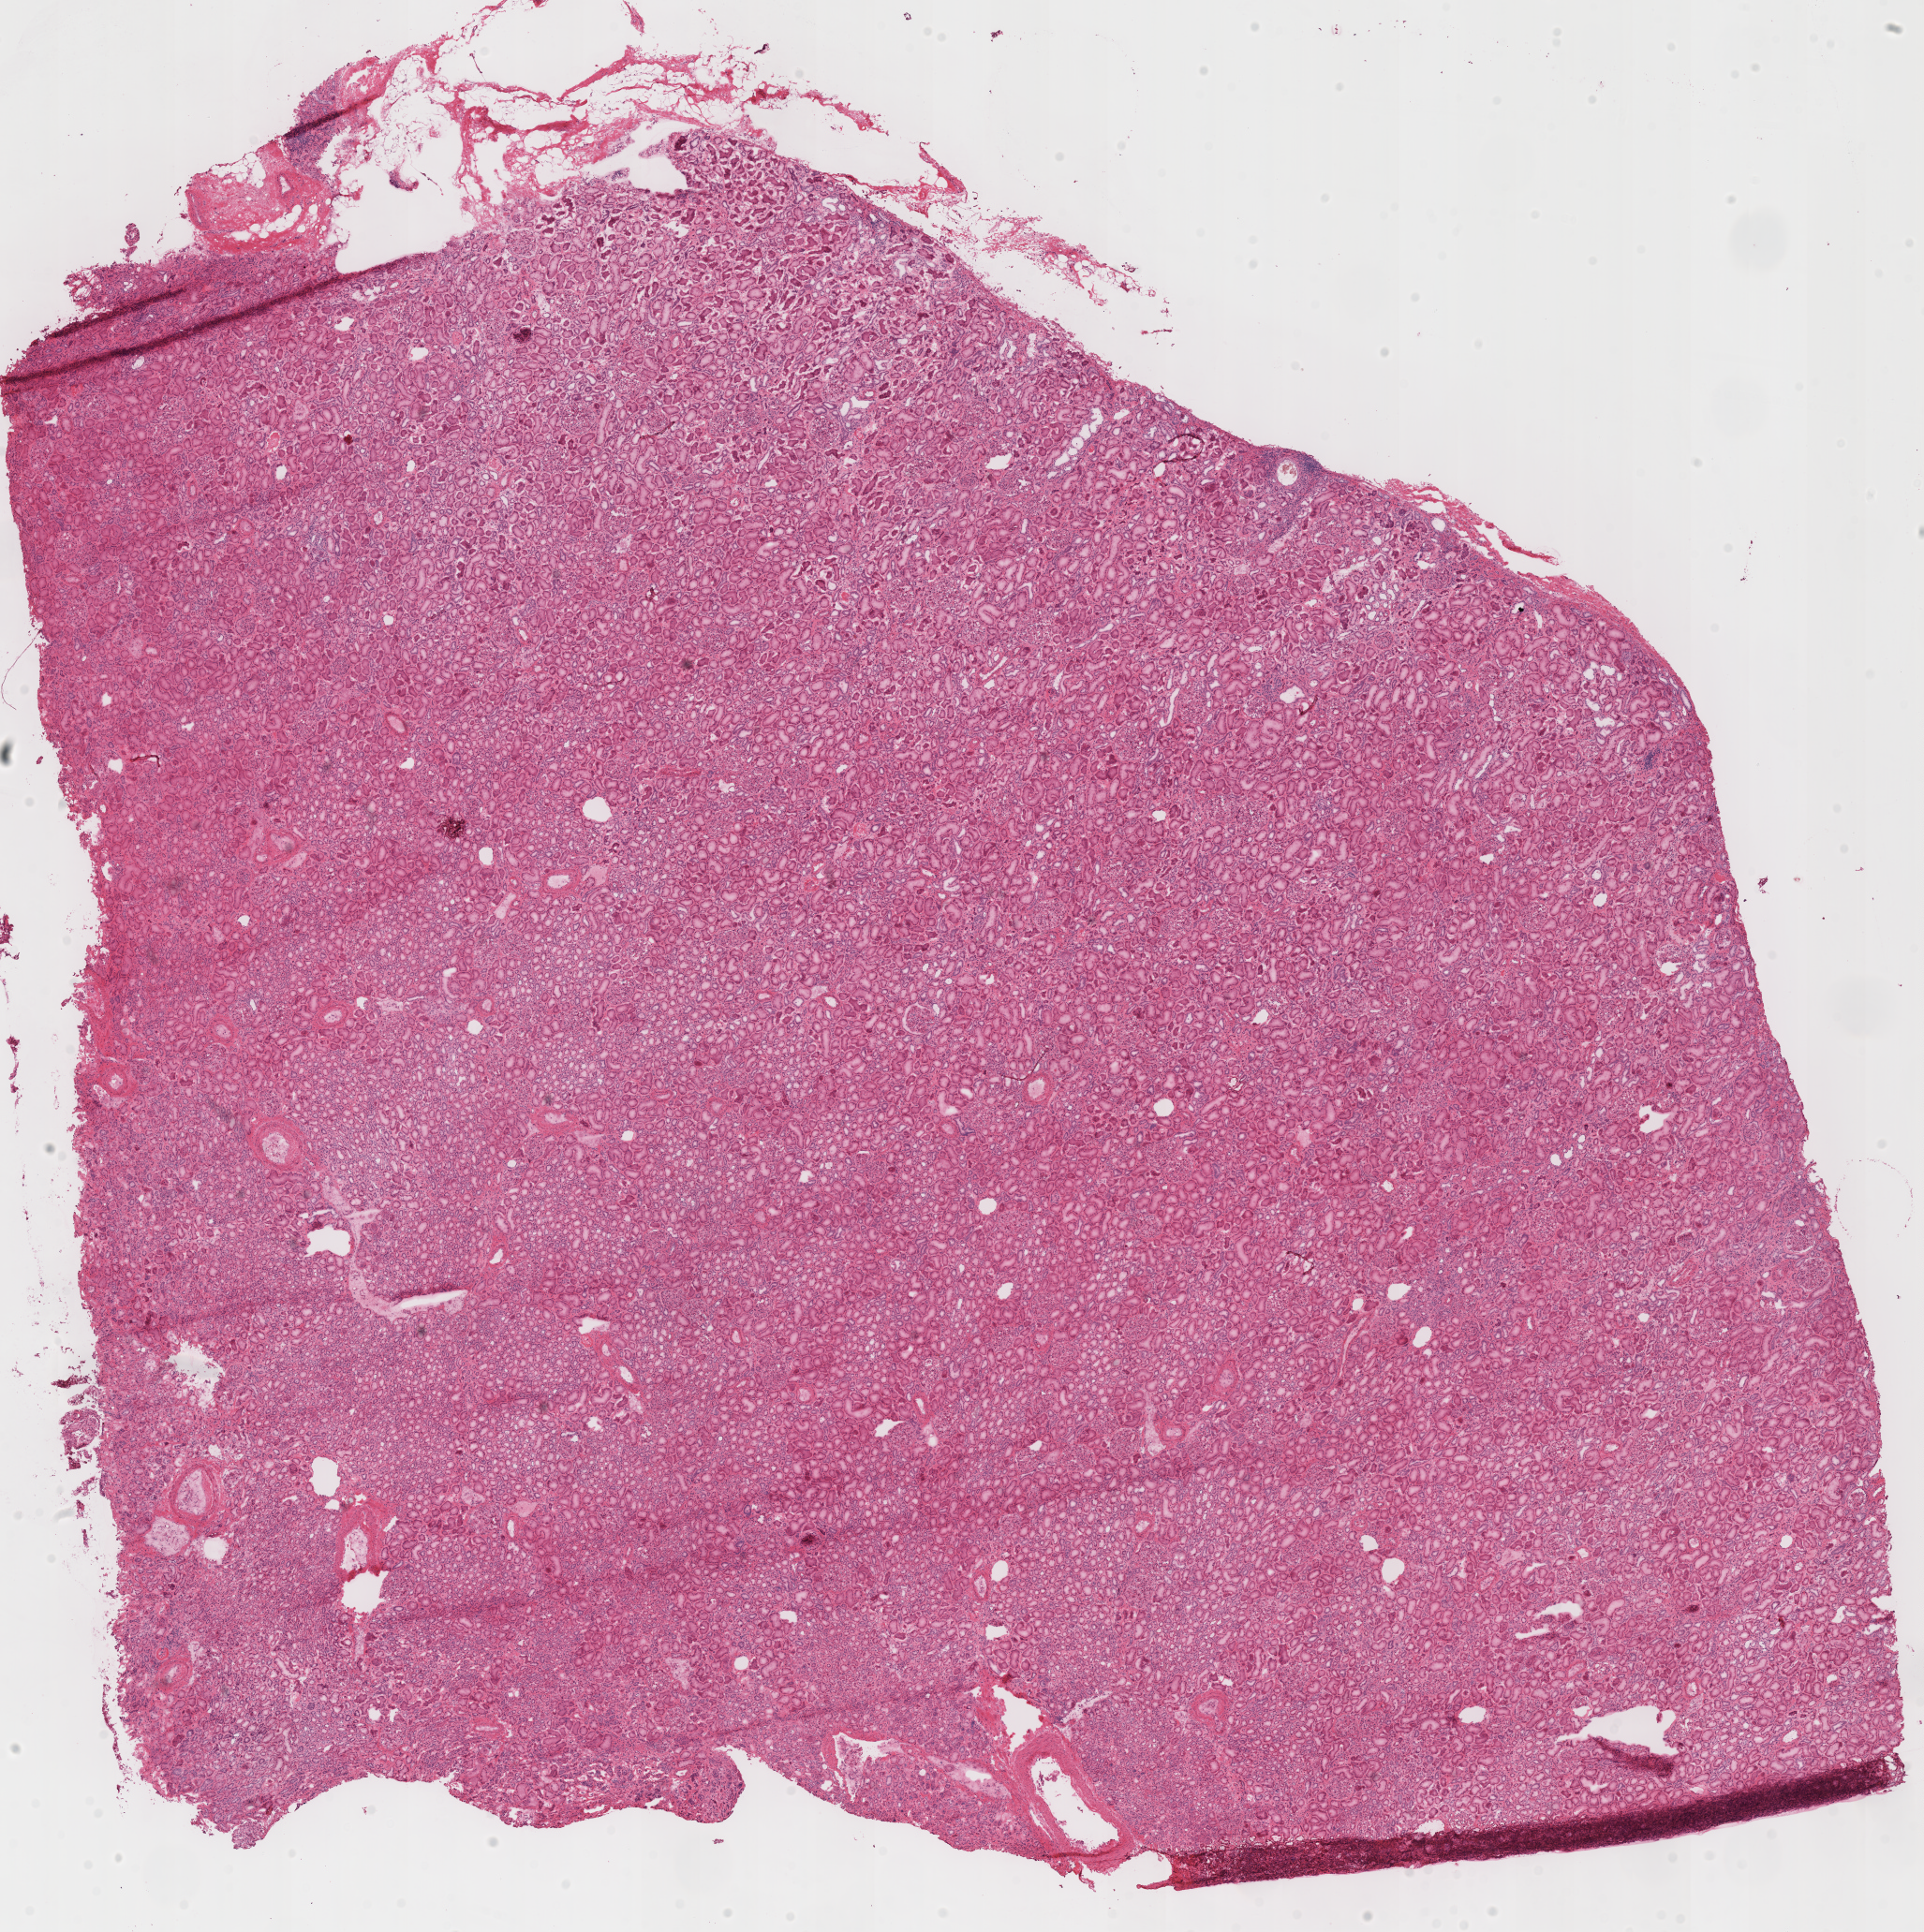
Digitized H&E-stained tissue section (whole slide) — shown as a low-resolution overview of the whole scanned area (about 16.2 x 16.2 mm, slide scanned at 40x), frozen section from the top of the tissue portion, sample: solid tissue normal (non-tumour tissue), kidney. Male patient; age at initial diagnosis 51 years.
This section: solid tissue normal (non-tumour) sample from the same patient. Patient diagnosis: Renal cell carcinoma, chromophobe type.